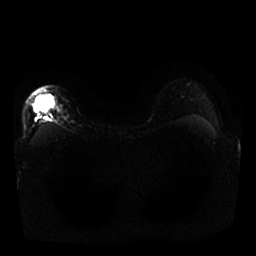
Breast MRI, one axial slice; position 20 of 25 along the scan axis; diffusion-weighted series; image 2 of 4 stored at this slice position (different b-values; order by instance number); 1.5 T; 4 mm slice thickness; 256 × 256 image matrix, field of view 340 × 340 mm. Female patient.
Outlined on this slice (manually delineated by an expert):
- tumour on diffusion-weighted imaging: bounding box (x1, y1, x2, y2) in pixels: (35, 98, 43, 108)